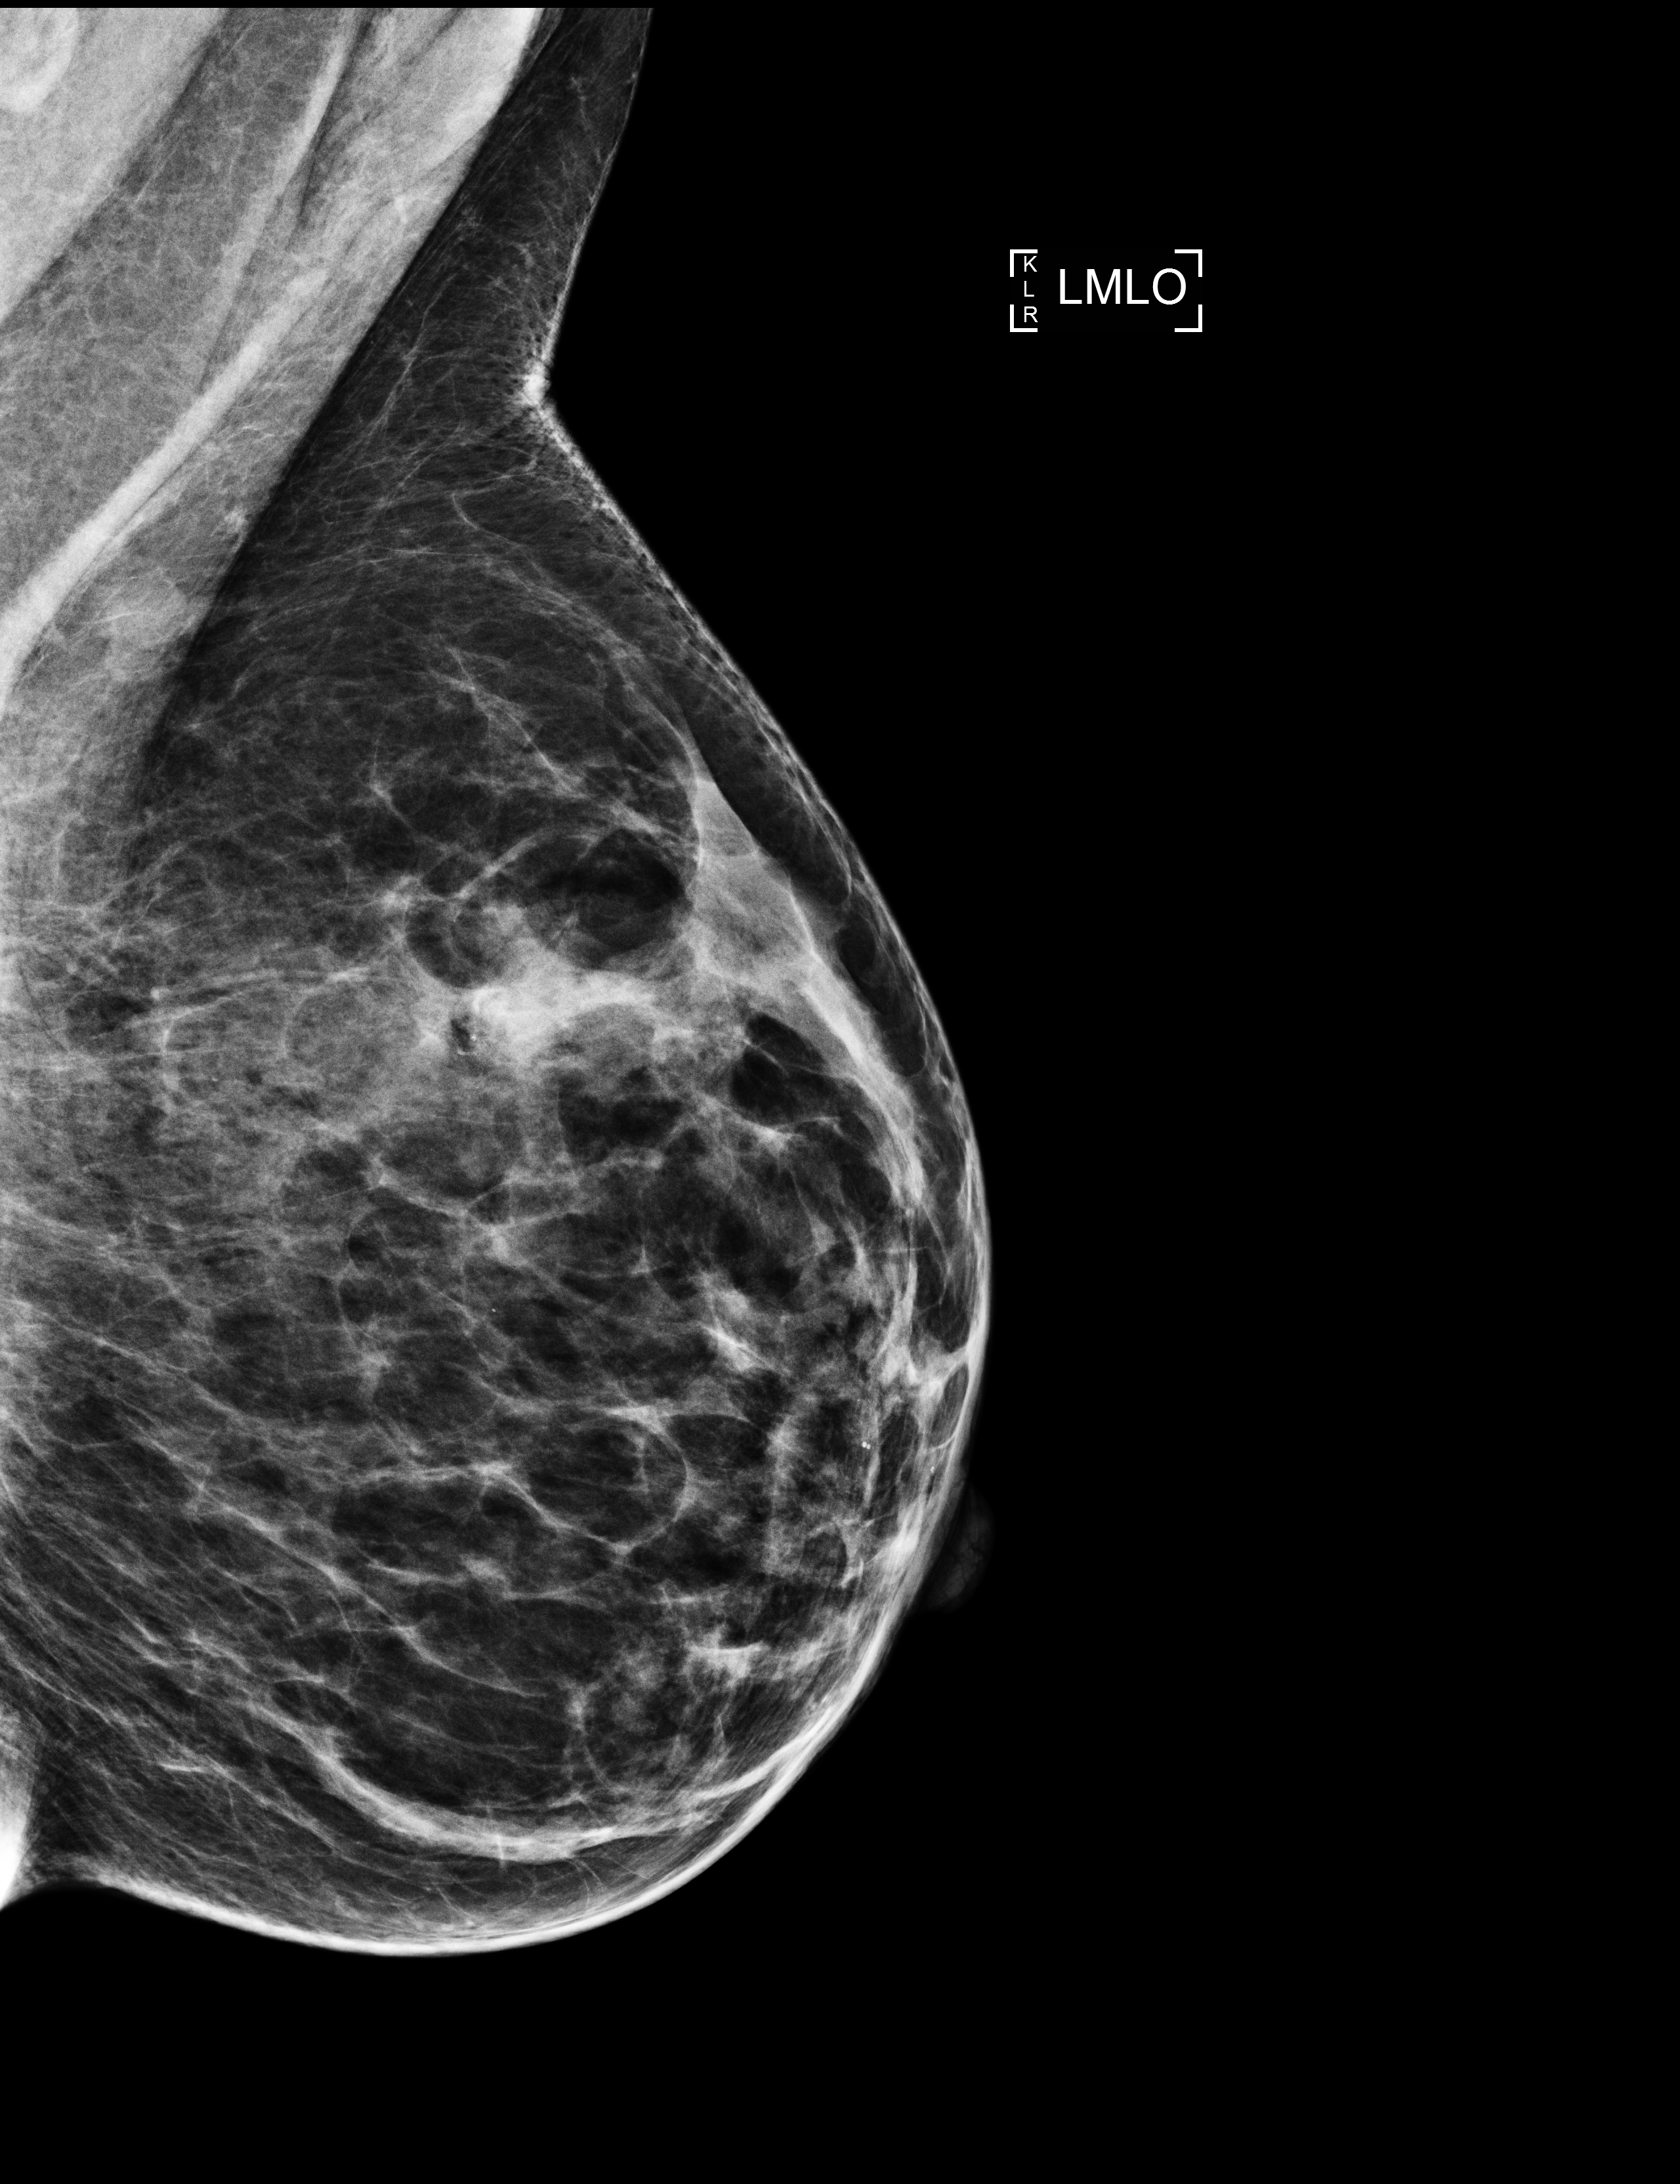
Full-field digital mammogram (FFDM), left breast, mediolateral oblique (MLO) view, screening examination. Female patient, age 62 years.
- BI-RADS breast density category at the screening exam (both breasts, scale 1–4): 3
- final BI-RADS assessment for this screening round (tomosynthesis exam, both breasts): category 2
- recall: no recall after this screen